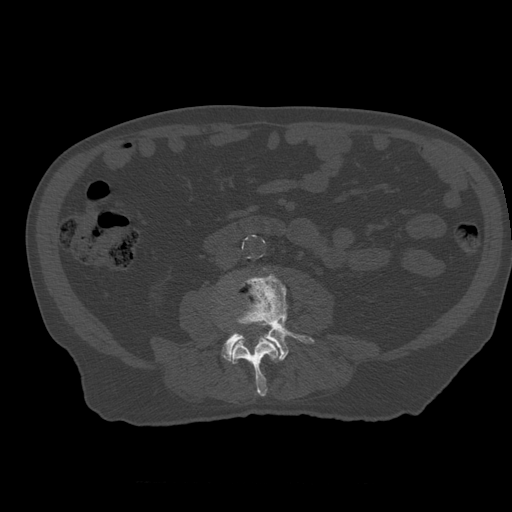
CT including the spine, one axial slice; position 177 of 399 along the scan axis; bone window (W 1800 / L 400 HU); 512 × 512 image matrix, field of view 407 × 407 mm. Patient age 73 years. Case-level facts recorded for this patient, not image findings: primary cancer: prostate; vertebrae with lytic lesions (as recorded): L2.
Annotated regions visible in this slice (semi-automatically segmented with operator editing):
- L3 vertebra: box from (x=218, y=301) to (x=282, y=397) px
- L4 vertebra: (x=222, y=274)–(x=314, y=362)